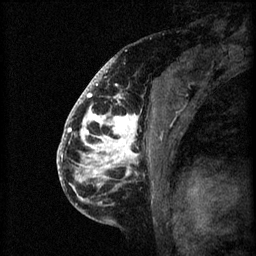
Breast MRI (dynamic contrast-enhanced), one sagittal slice. Position 38 of 60 along the scan axis. 3 images stored at this slice position (order not interpretable as contrast timing). 1.5 T. TE 4.2 ms, TR 8.2 ms. 2 mm slice thickness. 256 × 256 image matrix, field of view 180 × 180 mm. Patient: female, 41 years.
Annotated regions visible in this slice (semi-automatically segmented with operator editing):
- analysis volume of interest (the breast-tissue region the enhancement analysis was run in; not a lesion): bounding box <72,108,162,205> (left, top, right, bottom; pixels)
- tumour enhancement mask (voxels above the 70 % enhancement threshold inside the analysis volume of interest): <72,108,139,201>